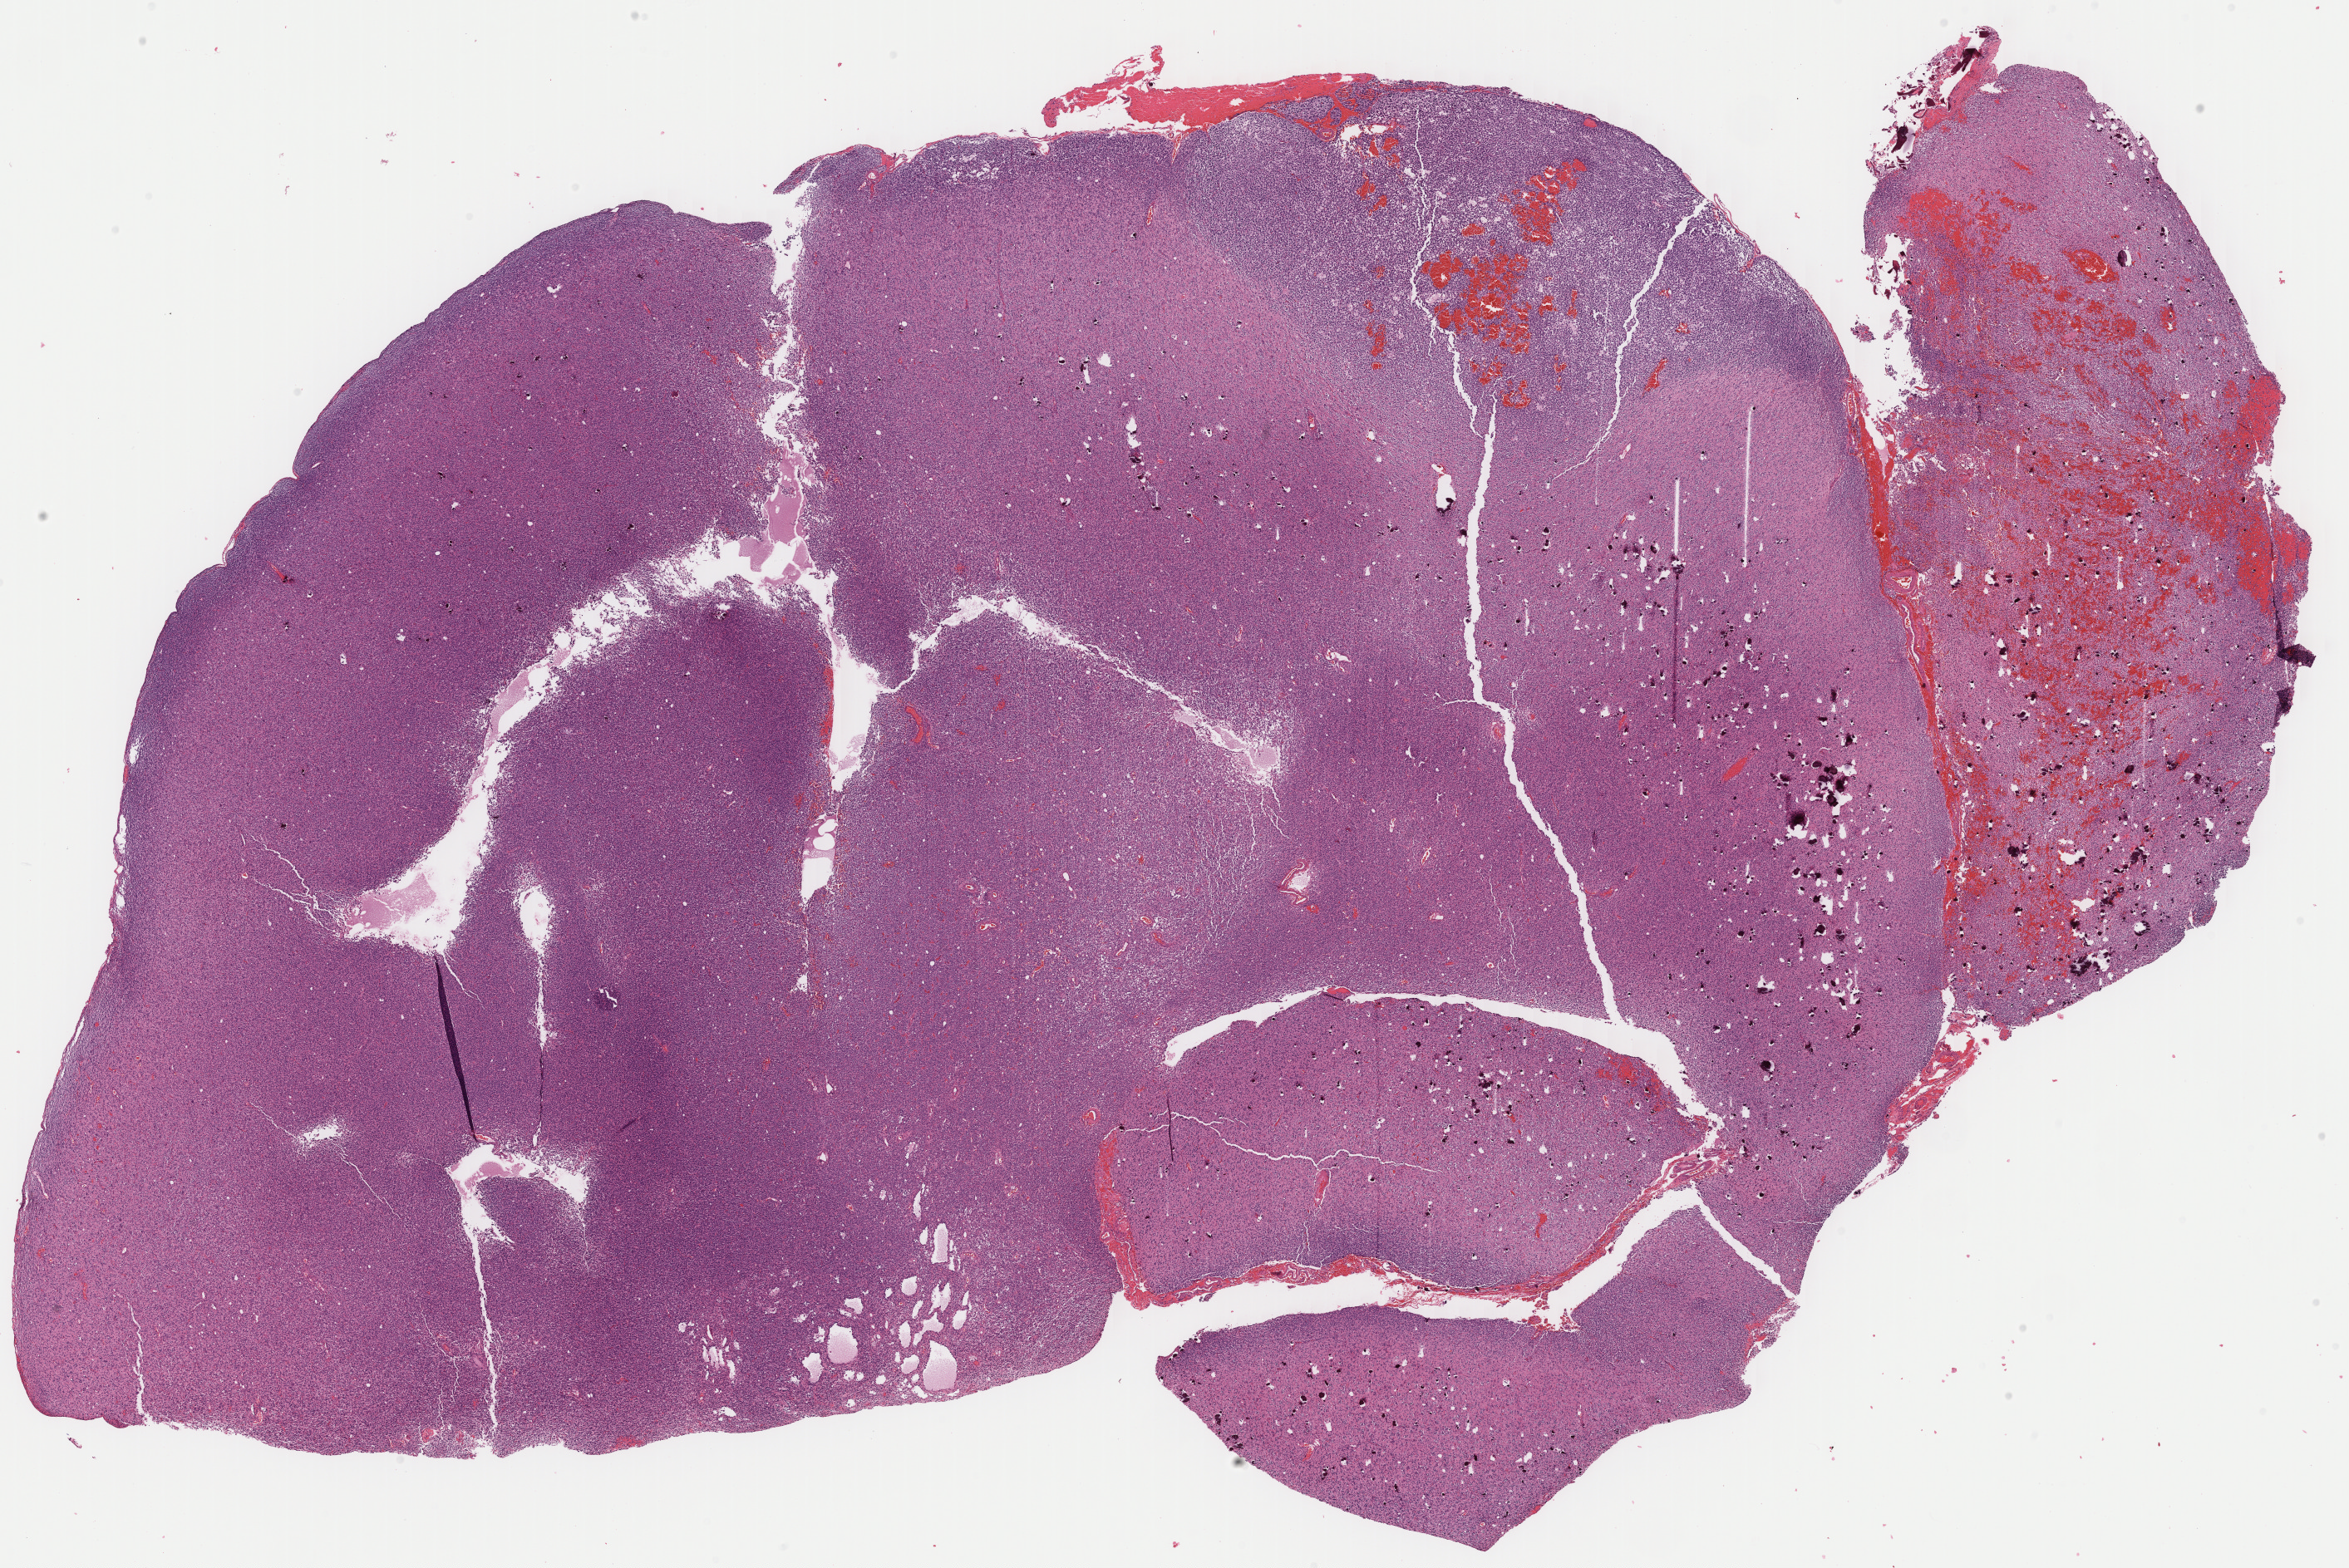
H&E whole-slide image, shown as a low-resolution overview of the whole scanned area (about 22.3 x 14.9 mm, slide scanned at 40x), formalin-fixed paraffin-embedded (FFPE) diagnostic section, primary tumour sample from the brain. Patient: male, age at initial diagnosis 34 years.
Pathologic diagnosis: Oligodendroglioma, anaplastic (frontal lobe).